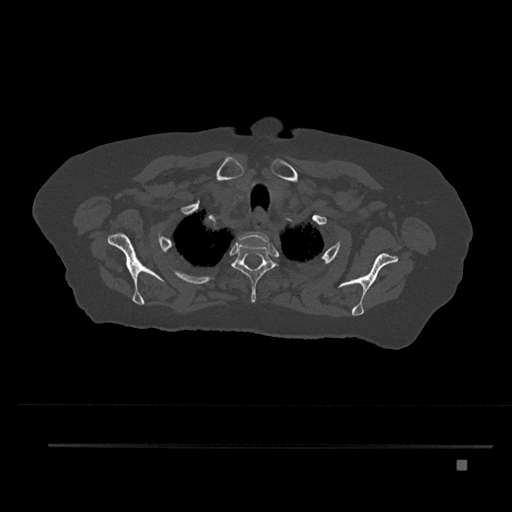
CT including the spine, one axial slice. Position 670 of 797 along the scan axis. Reconstruction kernel Br40s/3. 120 kVp. Bone window (W 1800 / L 400 HU). 512 × 512 image matrix, field of view 437 × 437 mm. Female patient, age 76 years. From the clinical record (not read from this slice): primary cancer: lung.
Annotated regions visible in this slice (semi-automatic segmentation, software-assisted and operator-edited):
- T1 vertebra: bounding box [x1, y1, x2, y2] px = [239, 231, 269, 247]
- T2 vertebra: [231, 242, 278, 302]